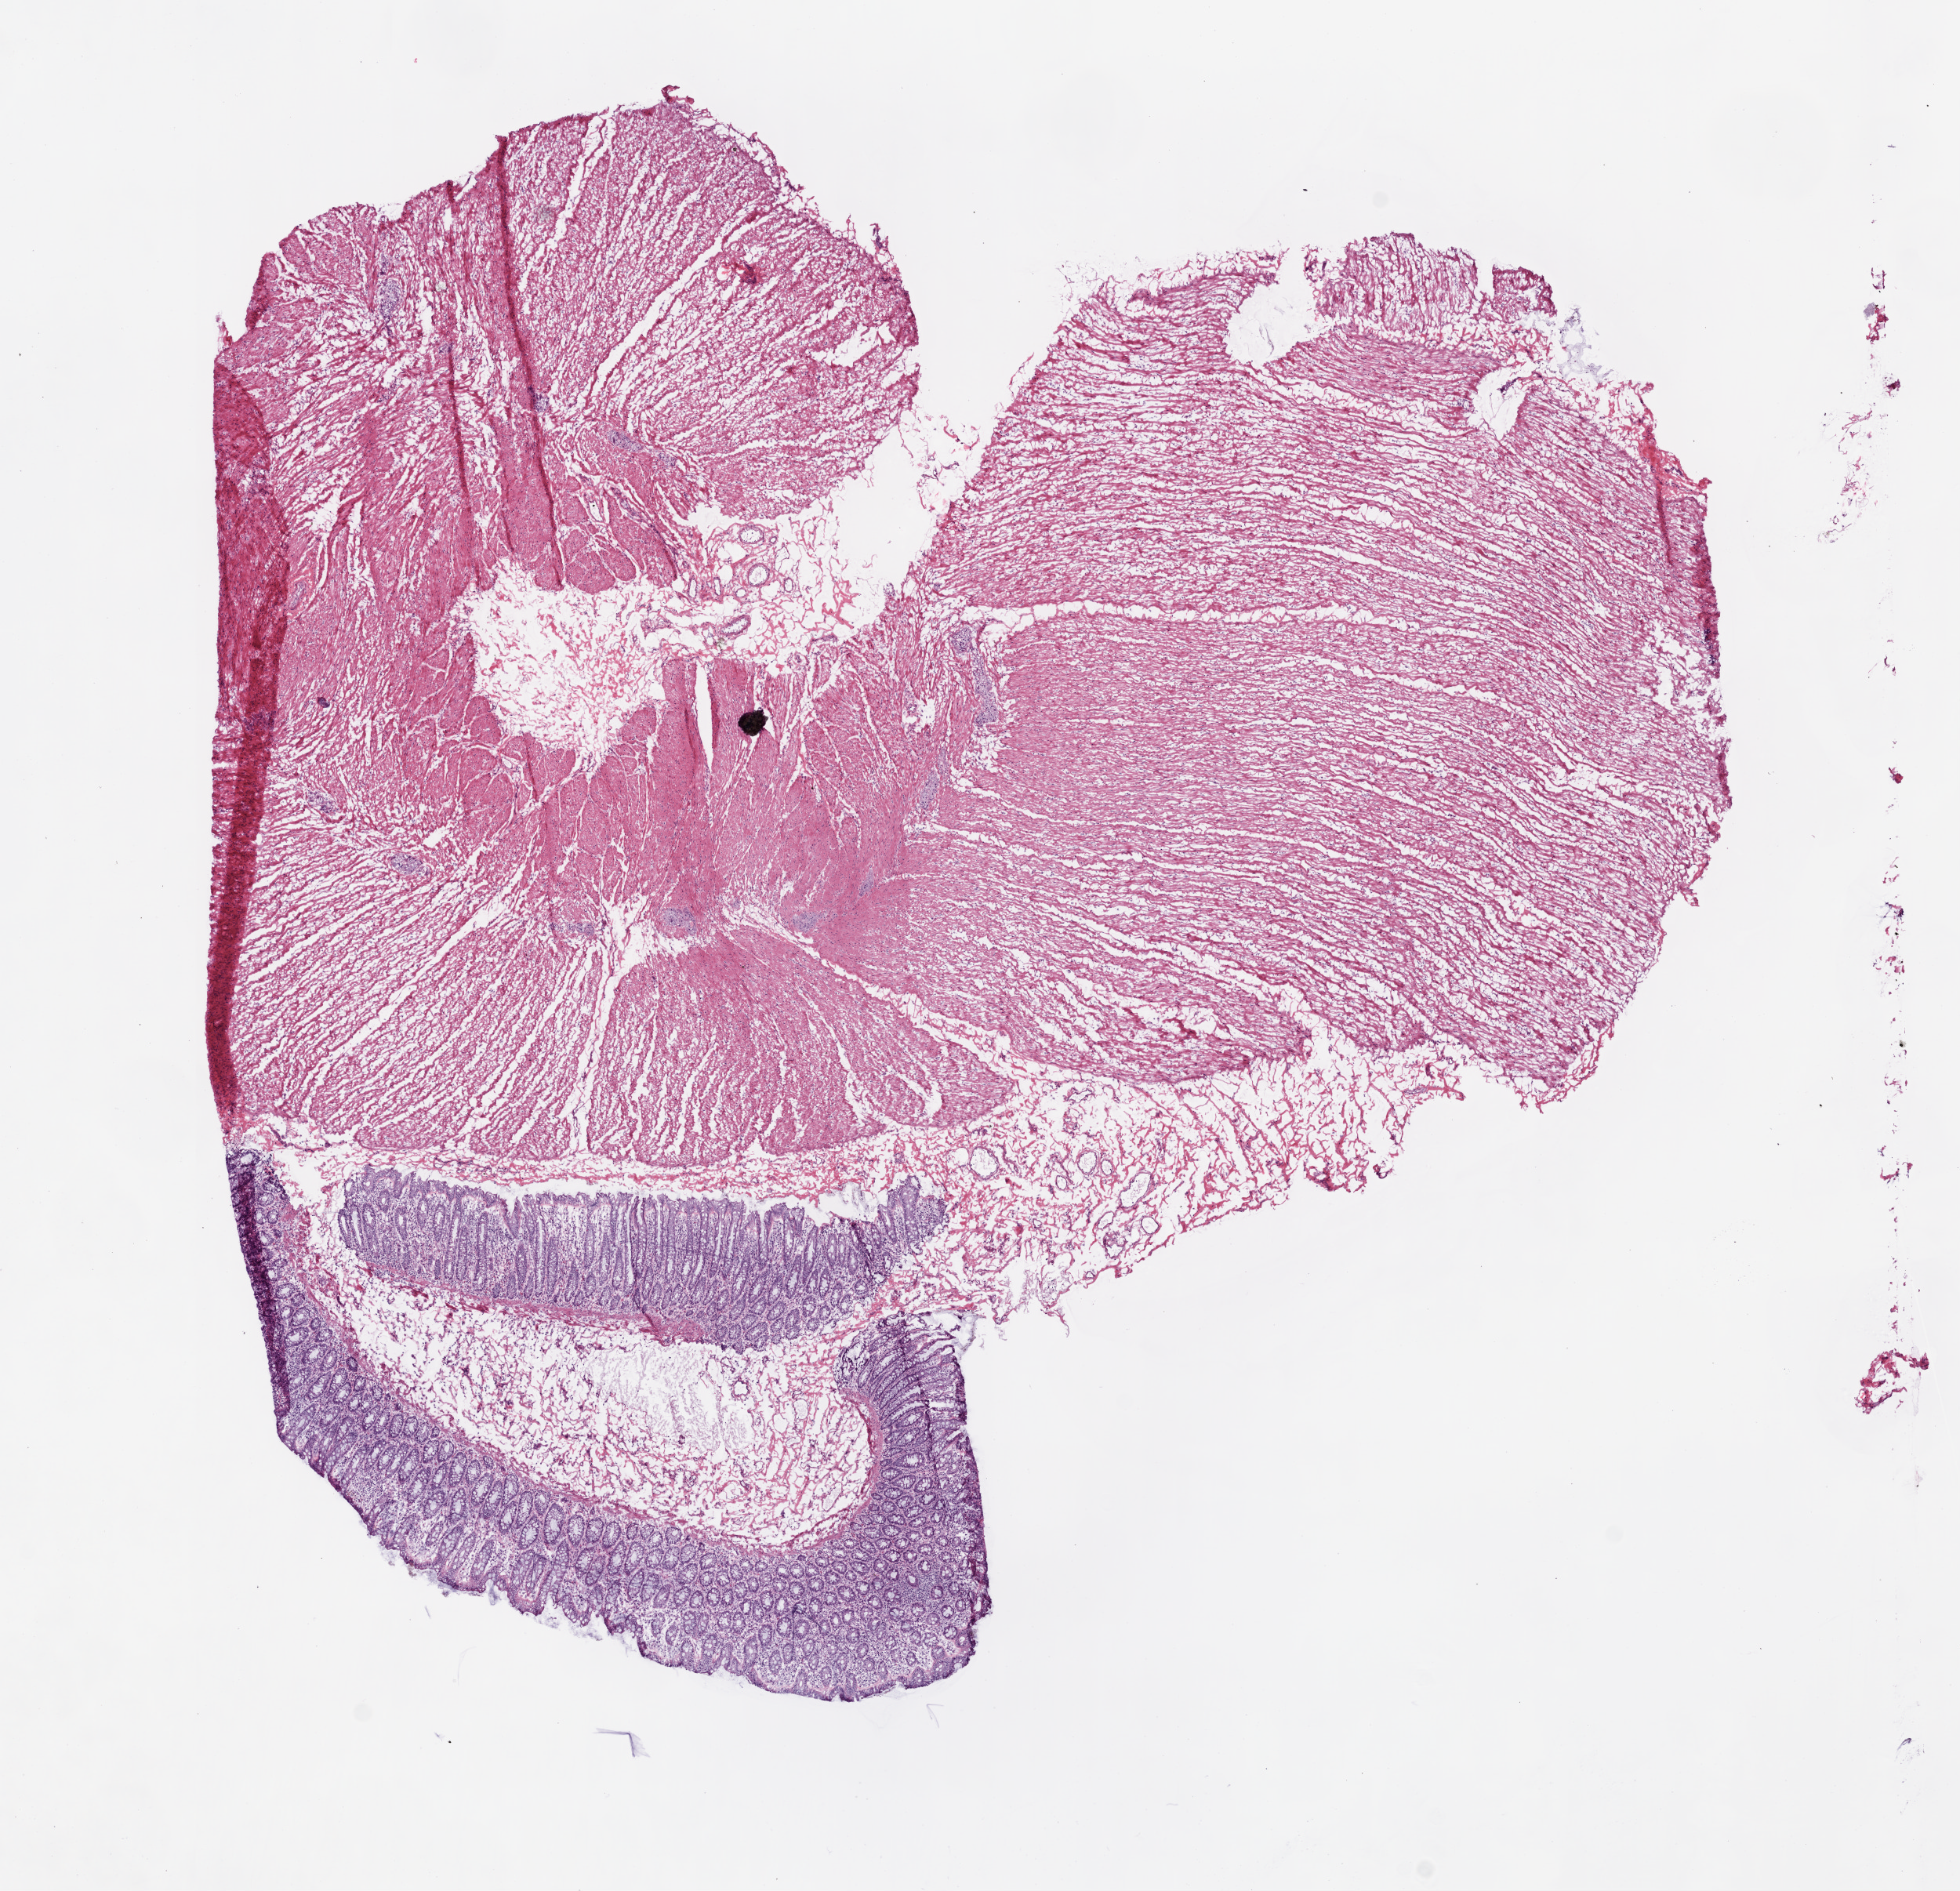
Hematoxylin and eosin (H&E) stained whole-slide image — whole scanned area (about 10.0 x 9.7 mm) shown as a low-resolution overview; frozen section; colon, solid tissue normal (non-tumour tissue) sample. Male patient; age at initial diagnosis 75 years.
* this section: solid tissue normal (non-tumour) sample from the same patient
* patient diagnosis: Adenocarcinoma, NOS